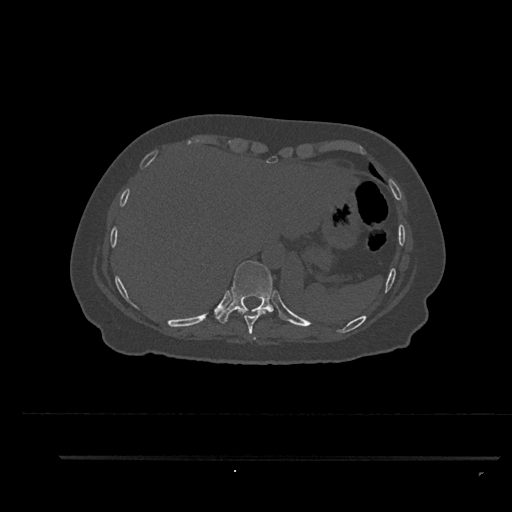
CT including the spine, one axial slice. Slice 386 of 797 in the series (ordered by position). Reconstruction kernel Br40s/3. 120 kVp. Bone window (W 1800 / L 400 HU). 512 × 512 image matrix, field of view 408 × 408 mm. Female patient, age 44 years. Case-level facts recorded for this patient, not image findings: primary cancer: renal.
Annotated regions visible in this slice (semi-automatic segmentation, software-assisted and operator-edited):
- T10 vertebra: bounding box [x1, y1, x2, y2] px = [215, 260, 282, 324]
- T9 vertebra: [238, 308, 266, 340]